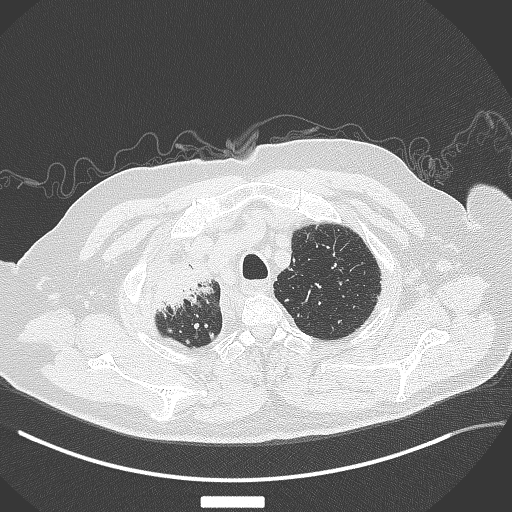
Chest CT, one axial slice; slice 318 of 384 in the series (ordered by position); reconstruction kernel B70f; 120 kVp; lung window (W 1500 / L -600 HU); 1 mm slice thickness; 512 × 512 image matrix. Male patient, age 69 years. From the clinical record (not read from this slice): clinical TNM (as recorded): T4 N3 M1.
Outlined on this slice (bounding box drawn by a radiologist):
- lung tumour (recorded histology: adenocarcinoma): bounding box [x1, y1, x2, y2] px = [151, 249, 223, 319]